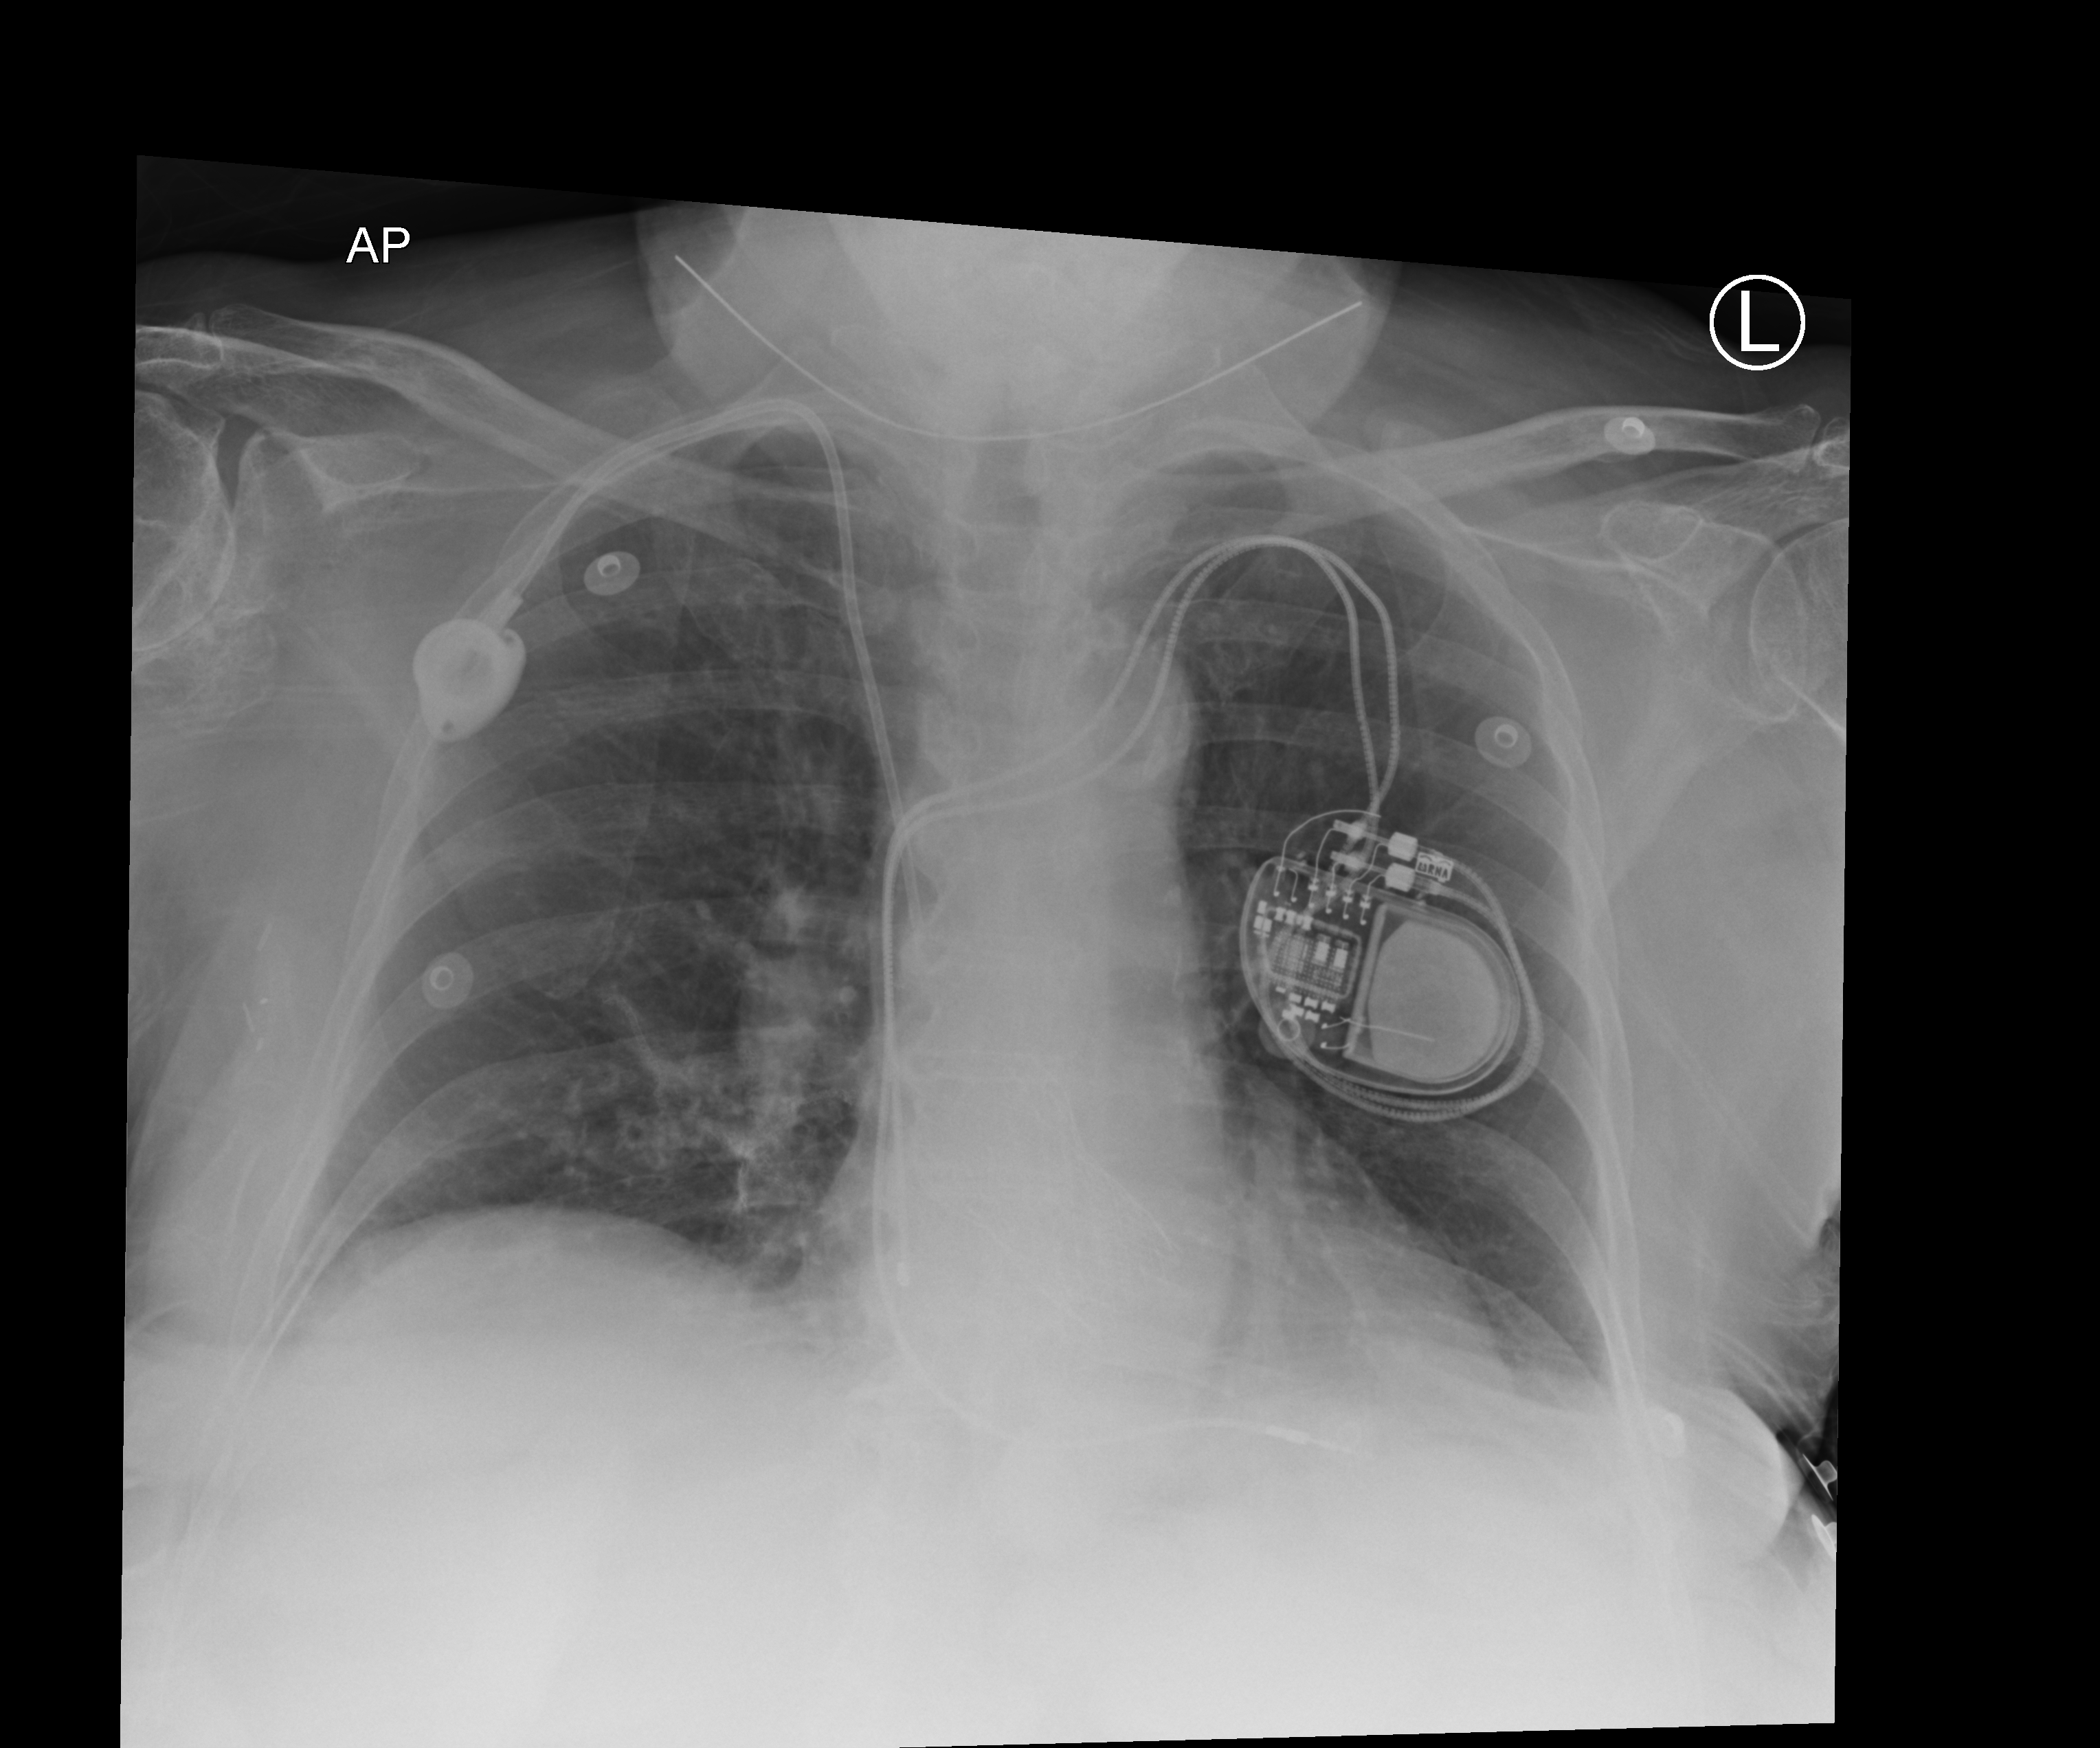
Chest X-ray (portable). Female patient hospitalised with COVID-19, age 75–90 years.
Admission-level facts for this patient (not findings on this image; timing relative to this image not recorded): admitted to intensive care during this hospital stay: no; mechanically ventilated during this hospital stay: no.